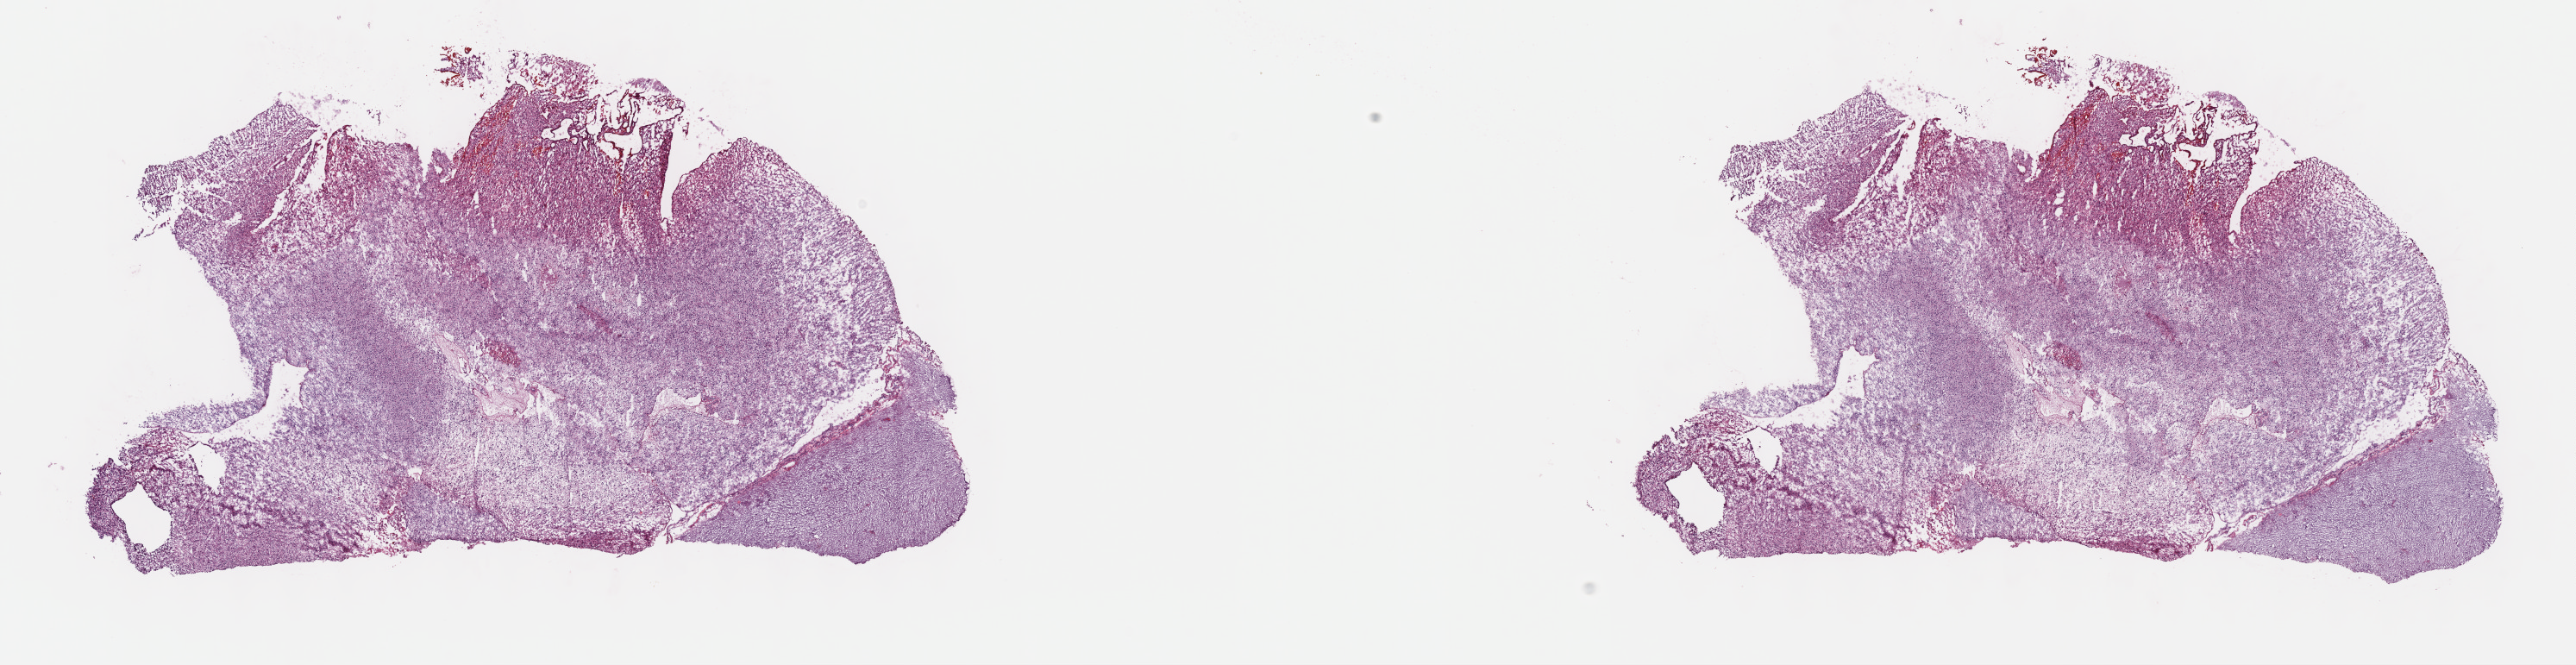
Digitized H&E-stained tissue section (whole slide) — a low-resolution overview of the entire scanned area, about 24.2 x 6.2 mm, frozen section, sample: primary tumour, brain. Male, age 52 years at initial diagnosis. Histologic grade: G3 (poorly differentiated). Slide review estimates, as recorded: tumour cells 60%, tumour nuclei 80%, normal cells 10%, stromal cells 30%, necrosis 0%. Infiltration values recorded for this section: lymphocyte infiltration 0%, monocyte infiltration 0%, neutrophil infiltration 0%.
Laterality: right. Pathologic diagnosis: Mixed glioma (cerebrum).